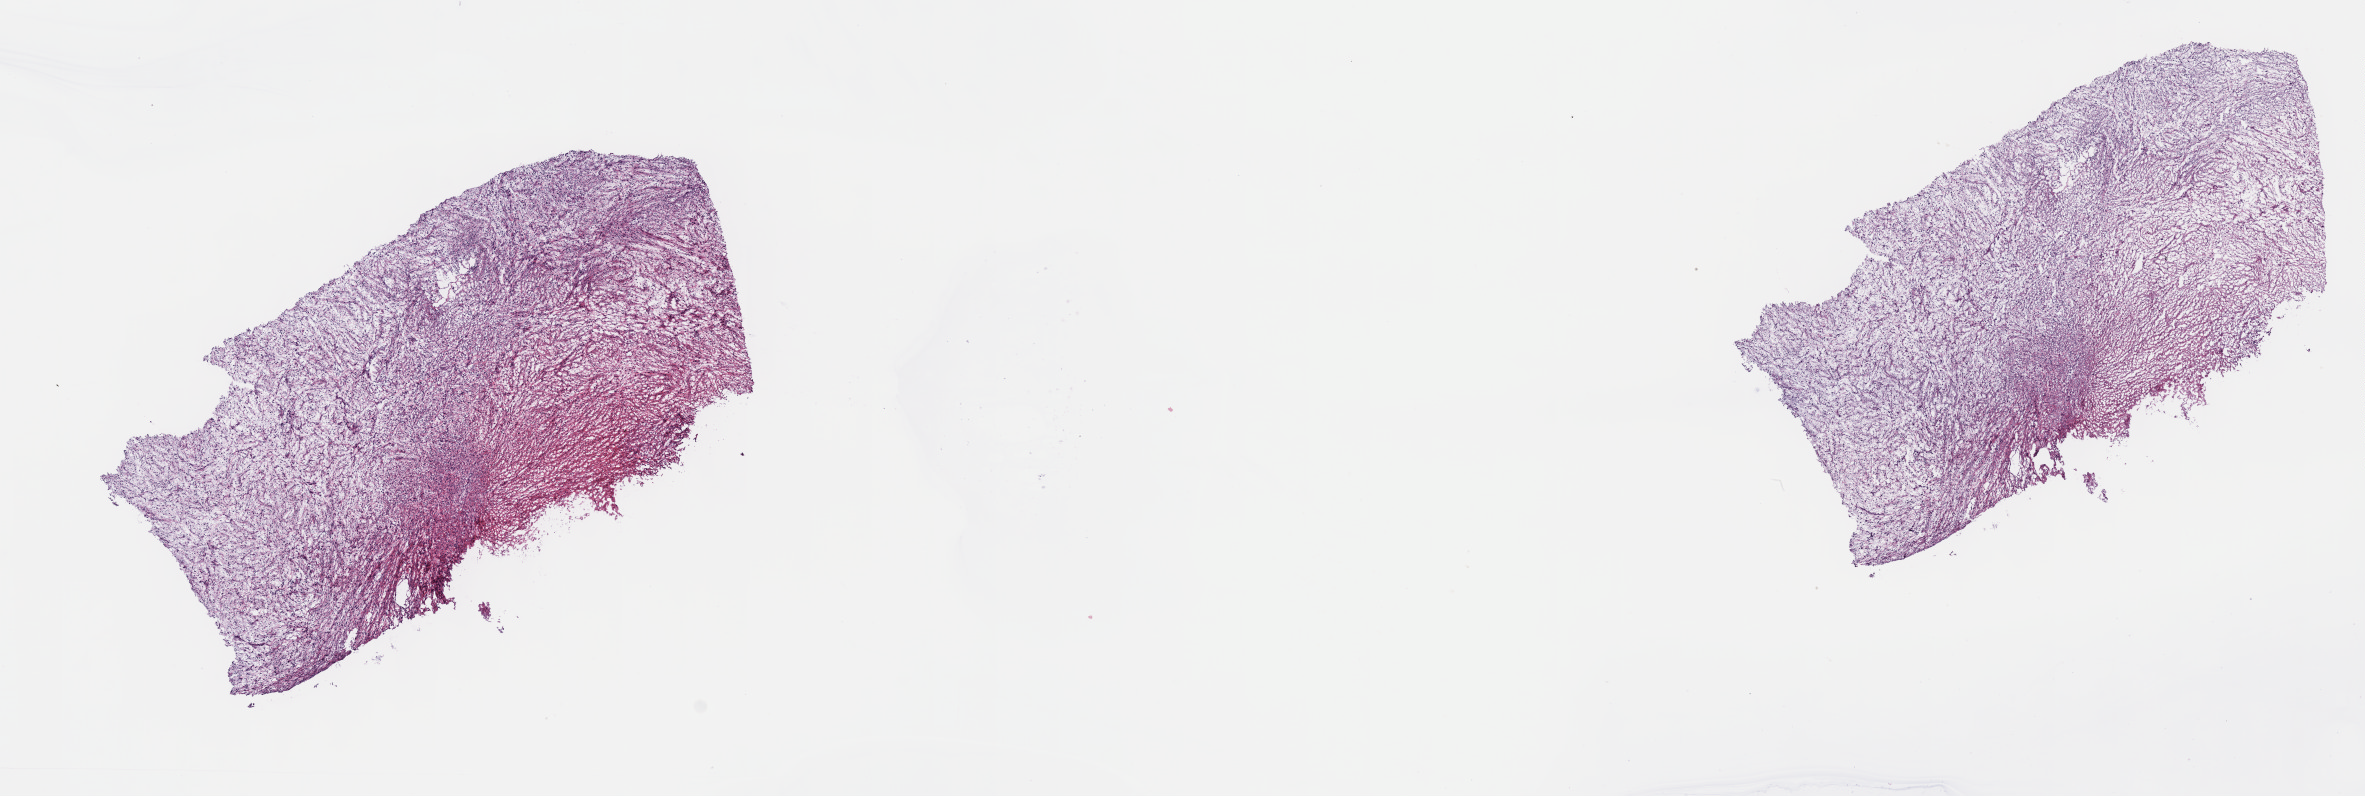
Whole-slide histology image, Hematoxylin and eosin (H&E) stained — shown as a low-resolution overview of the whole scanned area (about 19.1 x 6.4 mm, from a 40x scan), frozen section from the top of the tissue portion, sample: primary tumour, connective, subcutaneous and other soft tissues. Patient: male, age at initial diagnosis 68 years. Pathologist review of this section (percent, as recorded): tumour cells 100%, tumour nuclei 75%, normal cells 0%, stromal cells 0%, necrosis 0%. Infiltration values recorded for this section: lymphocyte infiltration 2%, monocyte infiltration 0%, neutrophil infiltration 0%.
* pathologic diagnosis: Dedifferentiated liposarcoma (connective, subcutaneous and other soft tissues of upper limb and shoulder)